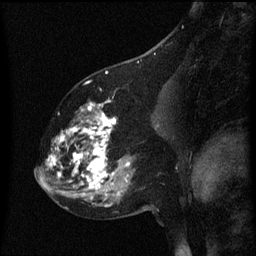
Breast MRI (dynamic contrast-enhanced), one sagittal slice. Slice 30 of 60 in the series (ordered by position). Dynamic contrast-enhanced series, image 2 of 3 at this slice position (ordered by acquisition). 1.5 T. TE 4.2 ms, TR 8 ms. 2 mm slice thickness. 256 × 256 image matrix, field of view 200 × 200 mm. Female patient, age 60 years.
Outlined on this slice (semi-automatic segmentation, software-assisted and operator-edited):
- analysis volume of interest (the breast-tissue region the enhancement analysis was run in; not a lesion): bounding box <49,100,158,197> (left, top, right, bottom; pixels)
- tumour enhancement mask (voxels above the 70 % enhancement threshold inside the analysis volume of interest): <49,100,131,191>